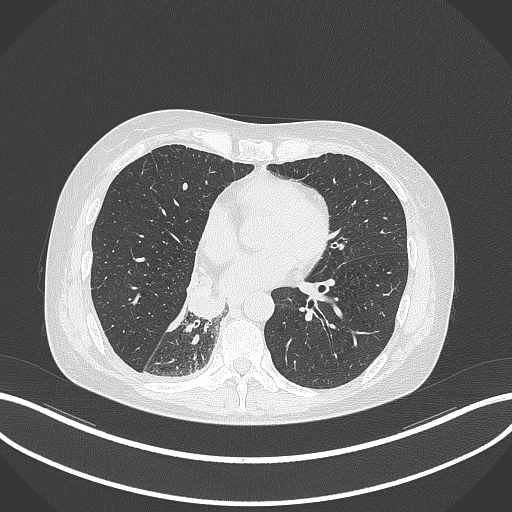
Chest CT, one axial slice. Position 126 of 329 along the scan axis. Reconstruction kernel B70f. Lung window (W 1500 / L -600 HU). 1 mm slice thickness. 512 × 512 image matrix, field of view 400 × 400 mm. Patient: female, 63 years. Case-level facts recorded for this patient, not image findings: clinical TNM (as recorded): T1c N0 M0.
Outlined on this slice (rectangle marked by the reading radiologist):
- lung tumour (recorded histology: adenocarcinoma): box from (x=184, y=271) to (x=226, y=321) px